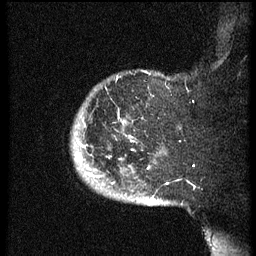
Breast MRI (dynamic contrast-enhanced), one sagittal slice. Position 52 of 60 along the scan axis. Dynamic contrast-enhanced series, image 2 of 3 at this slice position (ordered by acquisition). 1.5 T. TE 4.2 ms, TR 8.4 ms. 256 × 256 image matrix, field of view 200 × 200 mm. Patient: female, 38 years. From the clinical record (not read from this slice): setting: breast cancer imaged before/during neoadjuvant chemotherapy; receptor status: HER2-positive.
Outlined on this slice (semi-automatically segmented with operator editing):
- analysis volume of interest (the breast-tissue region the enhancement analysis was run in; not a lesion): bounding box (x1, y1, x2, y2) in pixels: (73, 74, 169, 202)
- tumour enhancement mask (voxels above the 70 % enhancement threshold inside the analysis volume of interest): (77, 146, 89, 175)